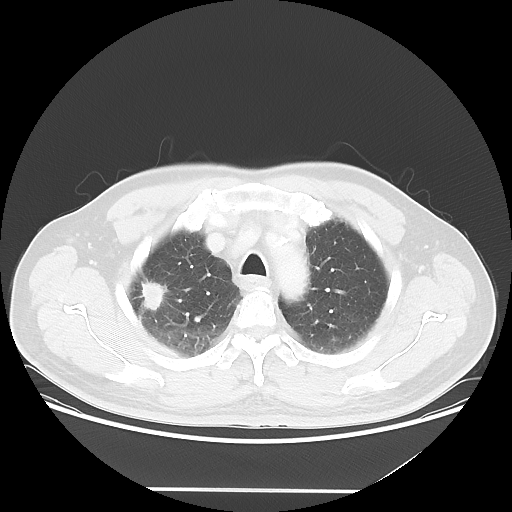
Chest CT, one axial slice. Slice 43 of 54 in the series (ordered by position). Reconstruction kernel LUNG. 120 kVp. Lung window (W 1500 / L -600 HU). 5 mm slice thickness. 512 × 512 image matrix. Male patient, age 65 years. From the clinical record (not read from this slice): clinical TNM (as recorded): T1c N1 M0.
Outlined on this slice (rectangle marked by the reading radiologist):
- lung tumour (recorded histology: adenocarcinoma): bounding box <134,275,170,321> (left, top, right, bottom; pixels)